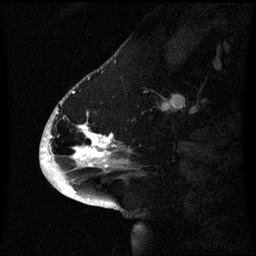
Breast MRI (dynamic contrast-enhanced), one sagittal slice. Position 21 of 60 along the scan axis. Dynamic contrast-enhanced series, image 2 of 3 at this slice position (ordered by acquisition). 1.5 T. TE 4.2 ms, TR 8.4 ms. 2.1 mm slice thickness. 256 × 256 image matrix, field of view 220 × 220 mm. Patient: female, 53 years. From the clinical record (not read from this slice): setting: breast cancer imaged before/during neoadjuvant chemotherapy; receptor status: HR-positive, HER2-negative.
Outlined on this slice (semi-automatically segmented with operator editing):
- analysis volume of interest (the breast-tissue region the enhancement analysis was run in; not a lesion): bounding box (x1, y1, x2, y2) in pixels: (52, 90, 130, 171)
- tumour enhancement mask (voxels above the 70 % enhancement threshold inside the analysis volume of interest): (57, 112, 111, 167)